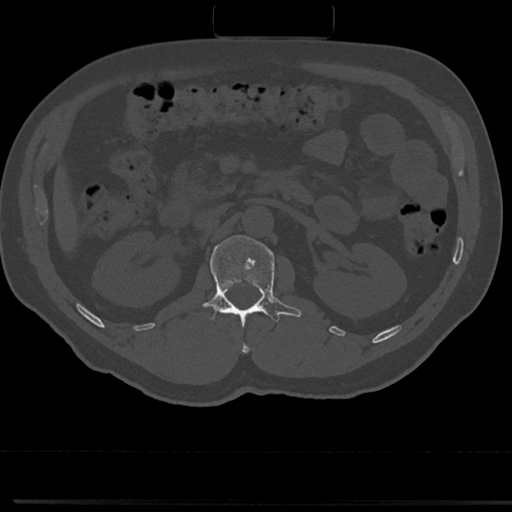
CT including the spine, one axial slice. Position 79 of 817 along the scan axis. Reconstruction kernel Br40s/3. Bone window (W 1800 / L 400 HU). 0.5 mm slice thickness. 512 × 512 image matrix. Male patient, age 61 years. Case-level facts recorded for this patient, not image findings: primary cancer: prostate.
Annotated regions visible in this slice (semi-automatically segmented with operator editing):
- L1 vertebra: box from (x=191, y=236) to (x=301, y=323) px